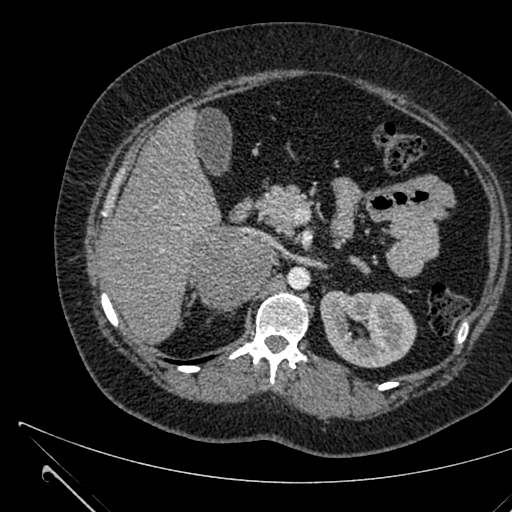
Contrast-enhanced abdominal CT, one axial slice. Position 399 of 731 along the scan axis. Soft-tissue window (W 400 / L 40 HU). 1 mm slice thickness. 512 × 512 image matrix. Female patient, age 36 years. From the clinical record (not read from this slice): diagnosis: adrenocortical carcinoma; tumour side: right adrenal; tumour size at pathology: 10 cm; Ki-67 index: 20 %; stage (as recorded): 4.
Structures marked on this image (semi-automatically segmented with operator editing):
- mass: box from (x=192, y=228) to (x=269, y=306) px